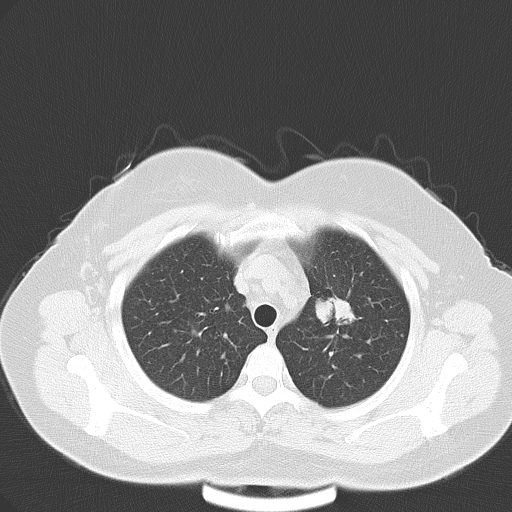
Chest CT, one axial slice. Position 44 of 57 along the scan axis. Reconstruction kernel B70f. 120 kVp. Lung window (W 1500 / L -600 HU). 5 mm slice thickness. 512 × 512 image matrix, field of view 353 × 353 mm. Patient: female, 53 years. Case-level facts recorded for this patient, not image findings: clinical TNM (as recorded): T1c N0 M1a.
Annotated regions visible in this slice (rectangle marked by the reading radiologist):
- lung tumour (recorded histology: adenocarcinoma): bounding box [x1, y1, x2, y2] px = [310, 289, 358, 329]